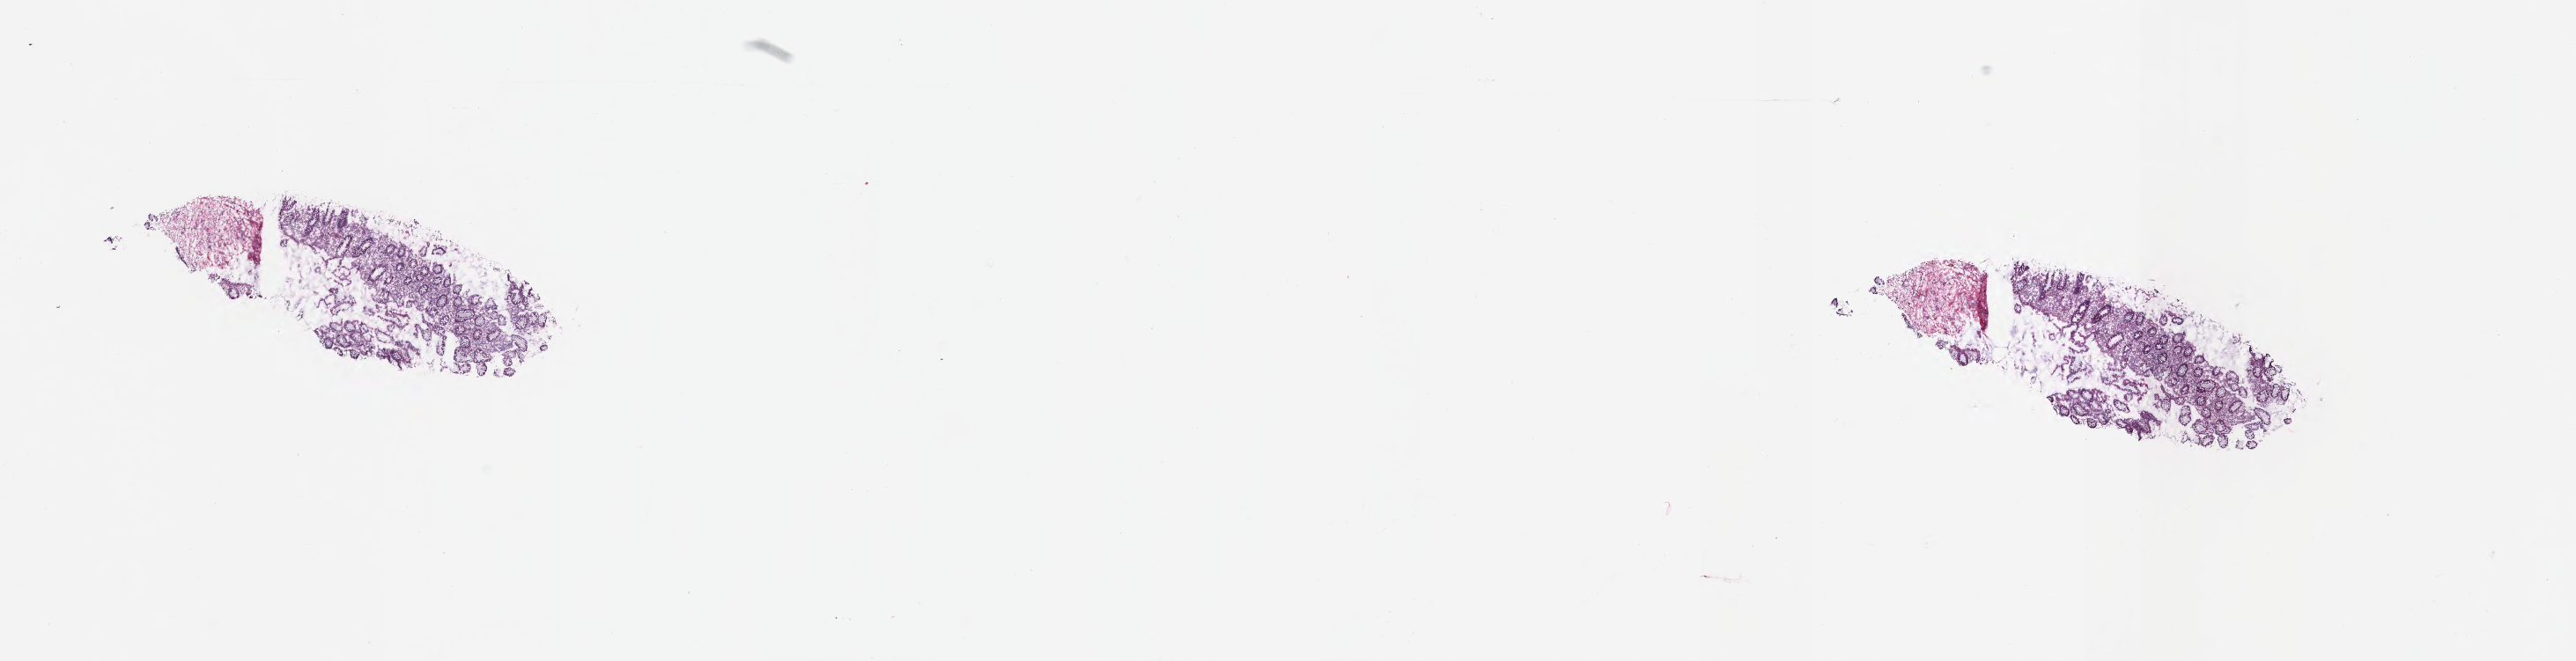
Whole-slide image, H&E stain — whole scanned area (about 23.6 x 6.1 mm) shown as a low-resolution overview. Cryosection. Non-tumor (normal tissue) sample from a patient with adenocarcinoma, NOS. Site: splenic flexure of colon. Patient sex: female. Pathologist review of this section (percent, as recorded): tumor cells 0%, tumor nuclei 0%, stromal cells 68%, necrosis 0%, normal cells 32%. Inflammatory infiltration, as recorded: lymphocyte infiltration 74%, monocyte infiltration 1%, neutrophil infiltration 0%.
- this section: non-tumor tissue sample; the patient's diagnosis is given above